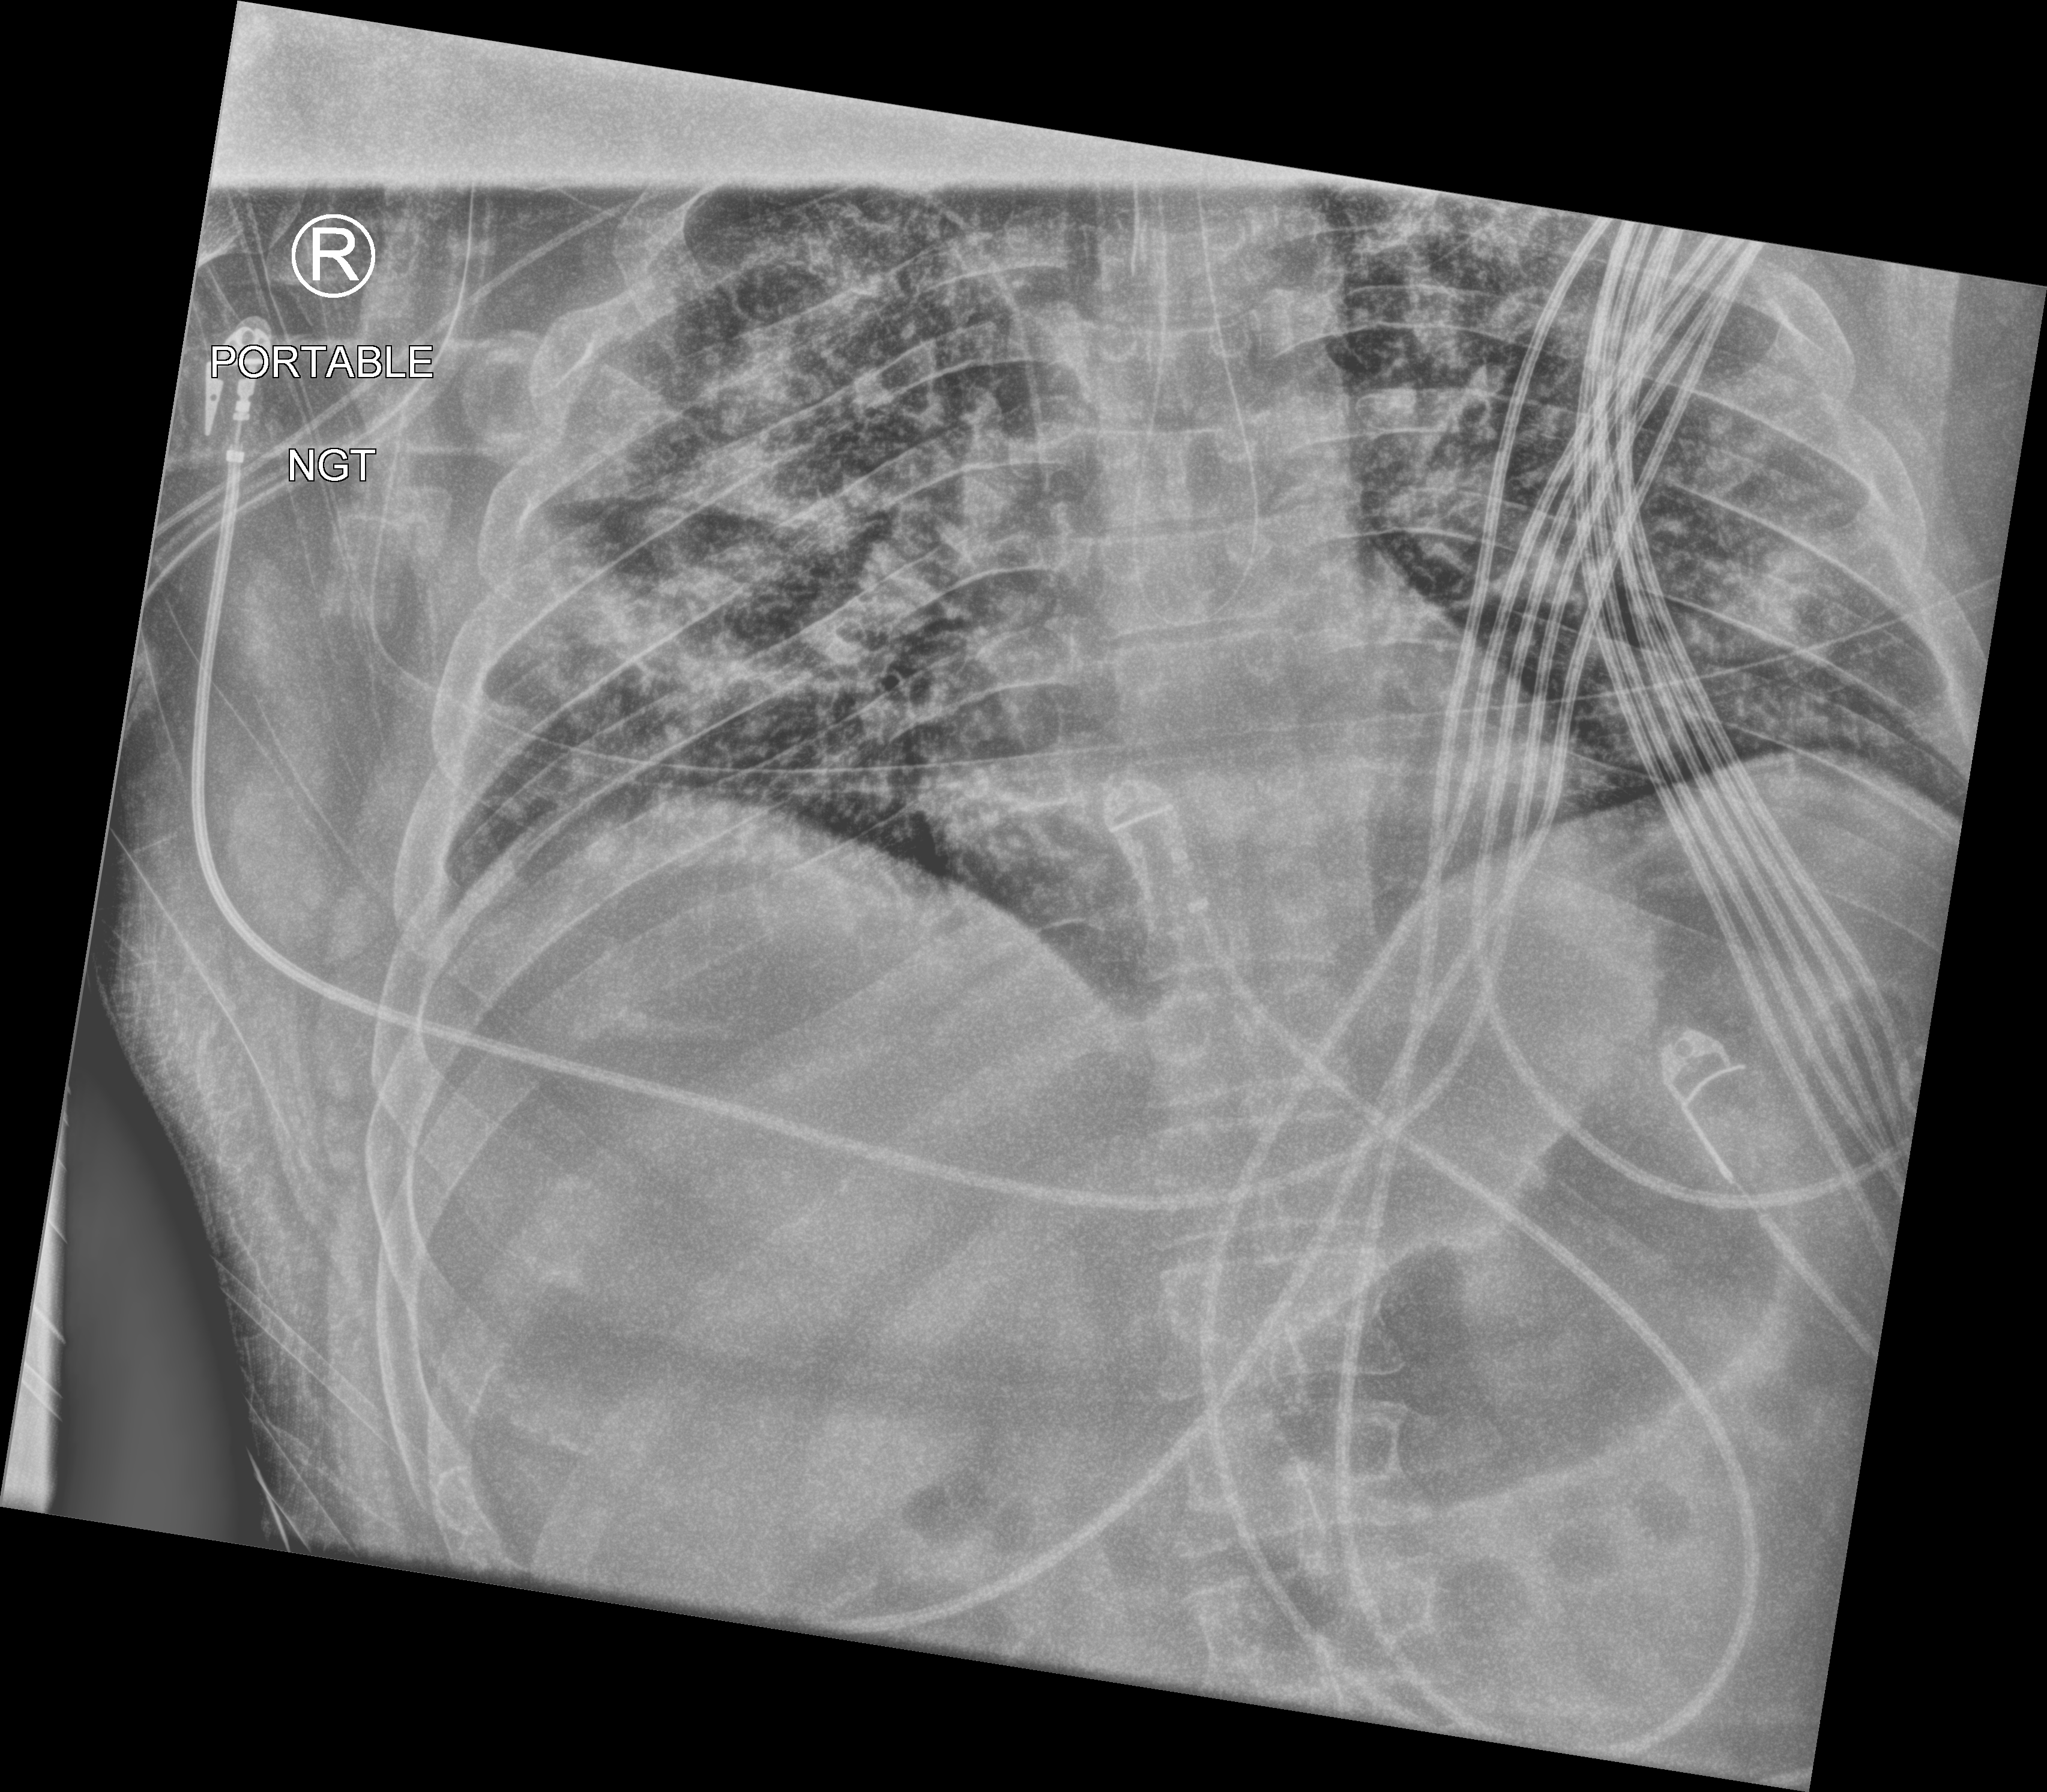
Portable chest radiograph, anteroposterior (AP) projection. Female patient hospitalised with COVID-19, age 18–59 years.
From the hospital-stay record, not from the radiograph (when in the stay this image was taken is not recorded): mechanically ventilated during this hospital stay: yes; admitted to intensive care during this hospital stay: yes.